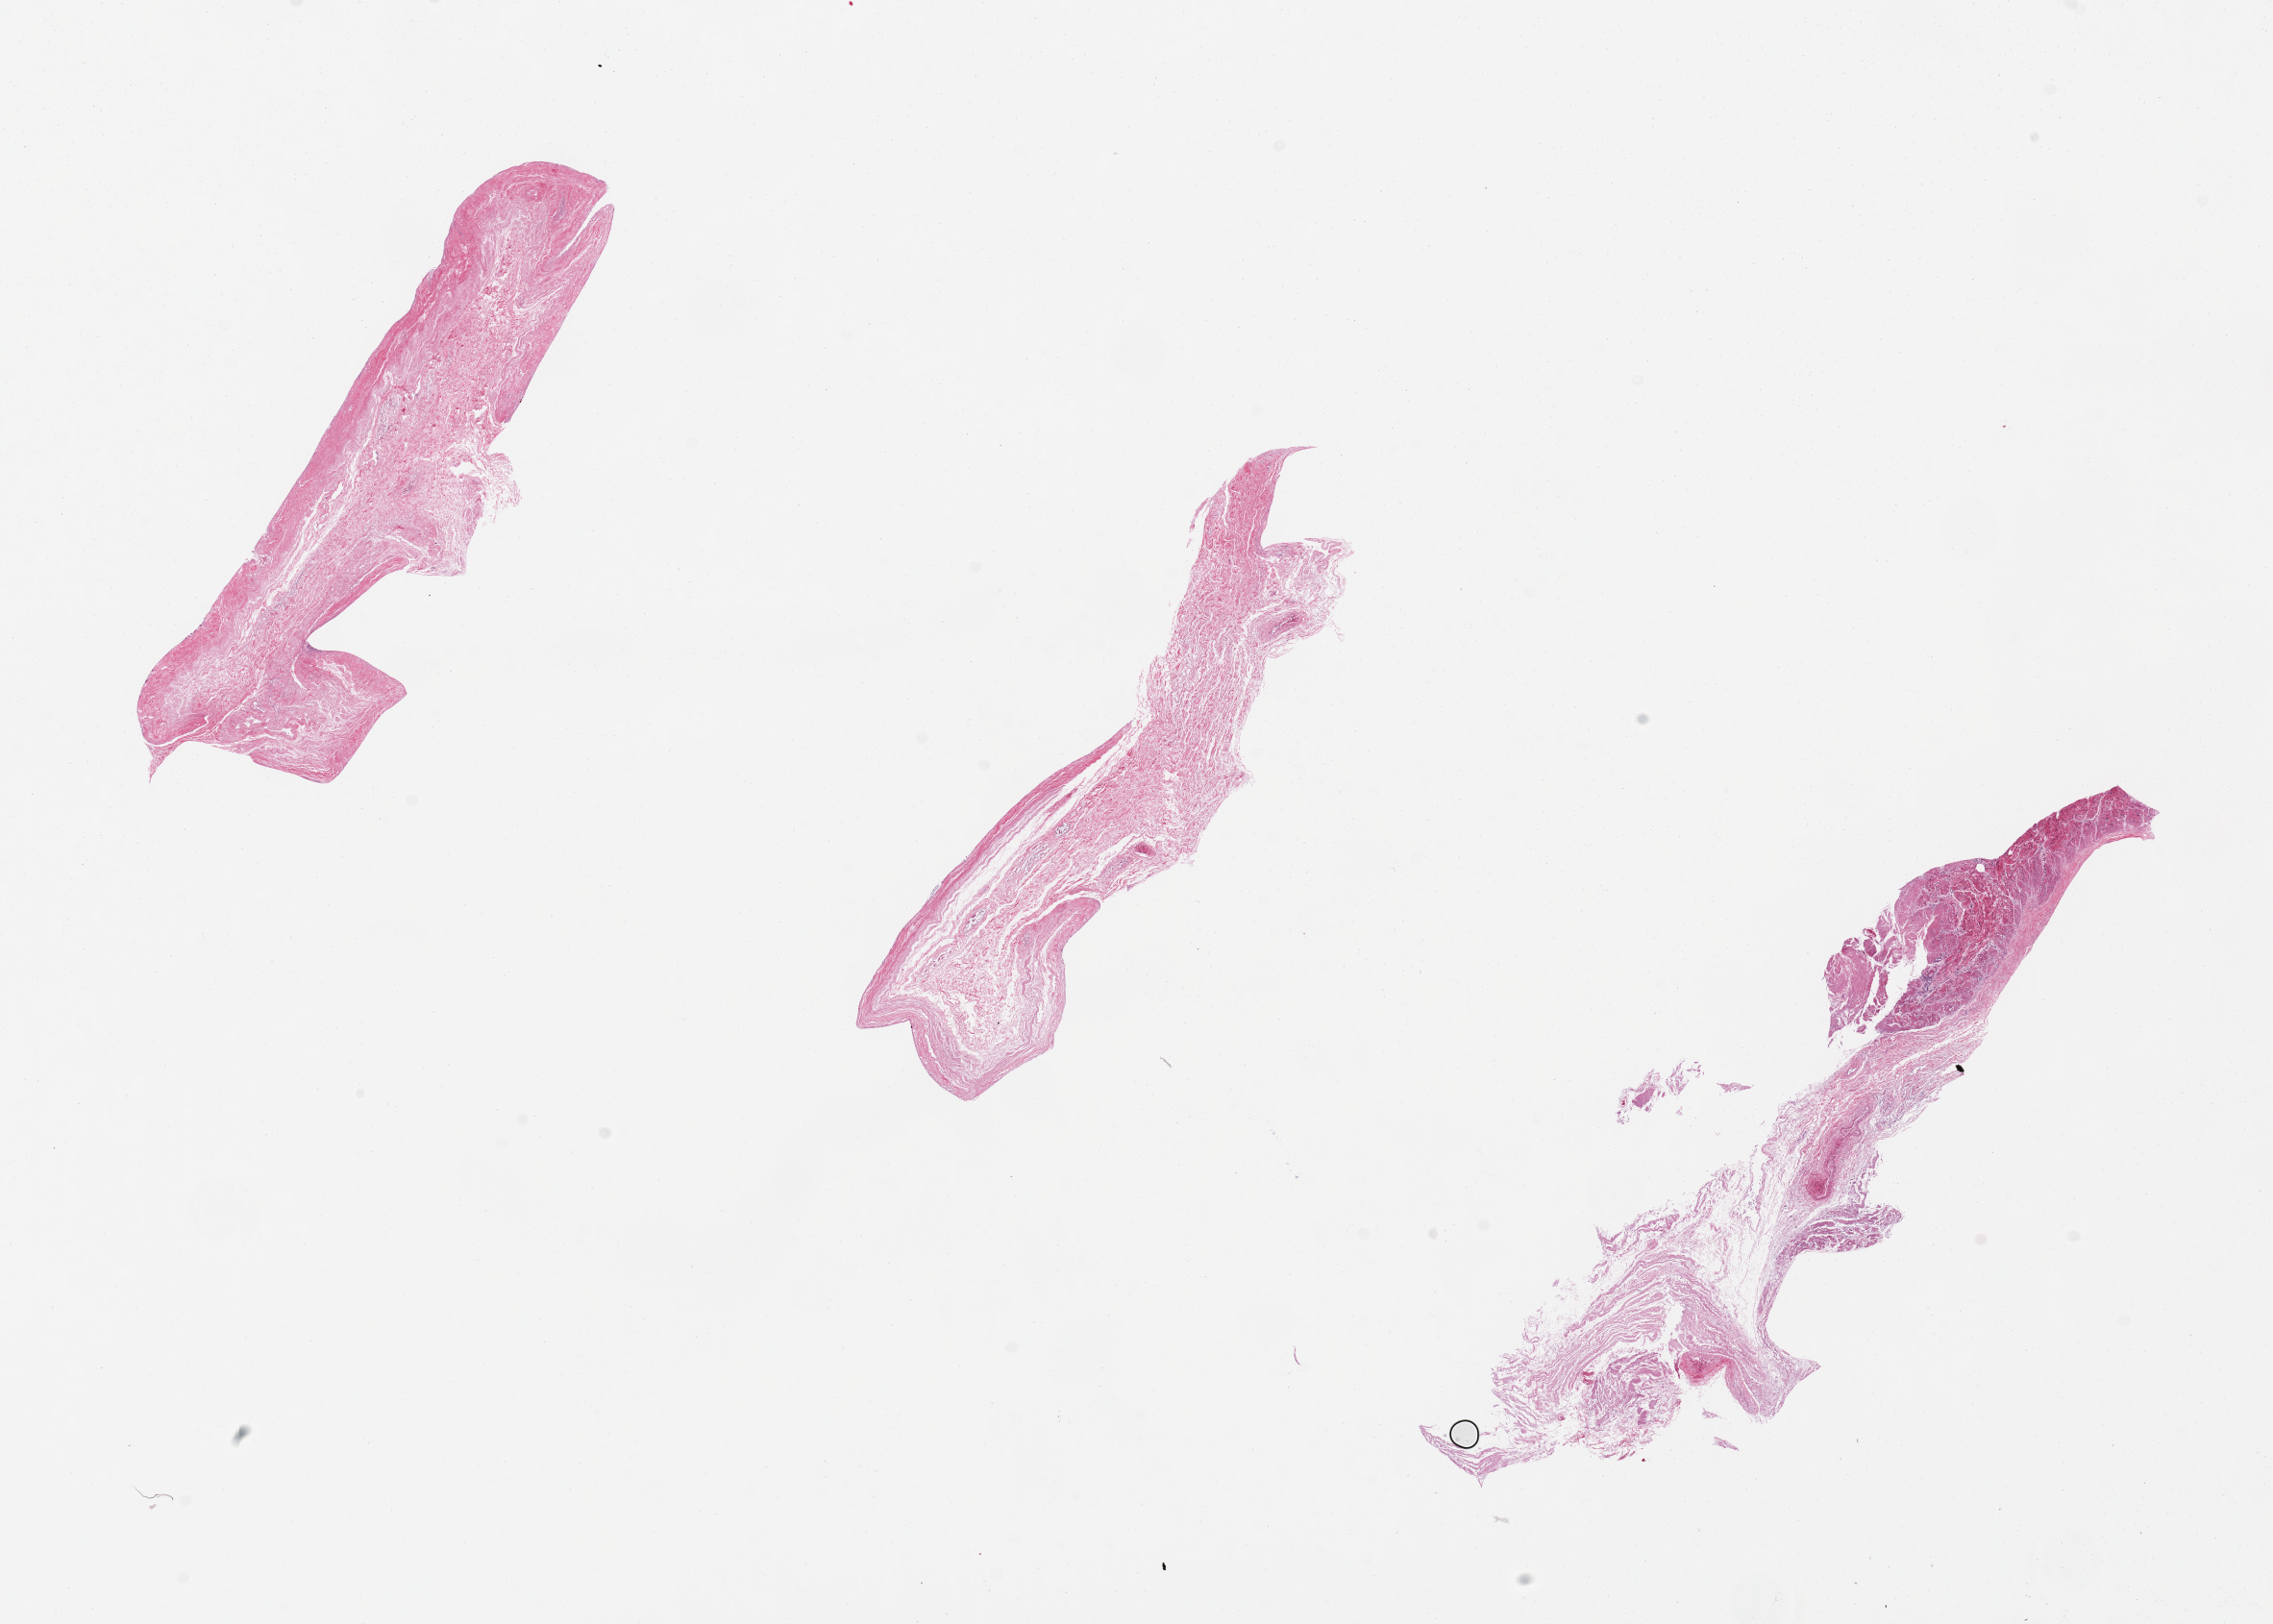
Digitized H&E-stained section, brightfield — shown as a low-resolution overview of the whole scanned area (about 18.7 x 13.4 mm), PAXgene-fixed, paraffin-embedded tissue, target tissue: esophageal mucous membrane, donor tissue sample.
- reviewer comment on this tissue sample: 3 pieces 5.6x1.2mm. No